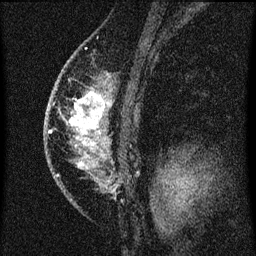
Breast MRI (dynamic contrast-enhanced), one sagittal slice; dynamic contrast-enhanced series, image 2 of 3 at this slice position (ordered by acquisition); 1.5 T; TE 4.2 ms, TR 8 ms; 2 mm slice thickness; 256 × 256 image matrix. Patient: female, 46 years.
Structures marked on this image (semi-automatic segmentation, software-assisted and operator-edited):
- analysis volume of interest (the breast-tissue region the enhancement analysis was run in; not a lesion): bounding box (x1, y1, x2, y2) in pixels: (54, 70, 114, 195)
- tumour enhancement mask (voxels above the 70 % enhancement threshold inside the analysis volume of interest): (69, 92, 110, 167)